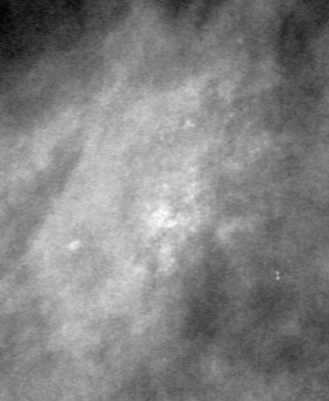
Region of interest cut from a scanned film mammogram (one marked finding); left breast; MLO view.
- Calcifications, morphology pleomorphic, distribution clustered; BI-RADS assessment category 4; pathology (as recorded): malignant.